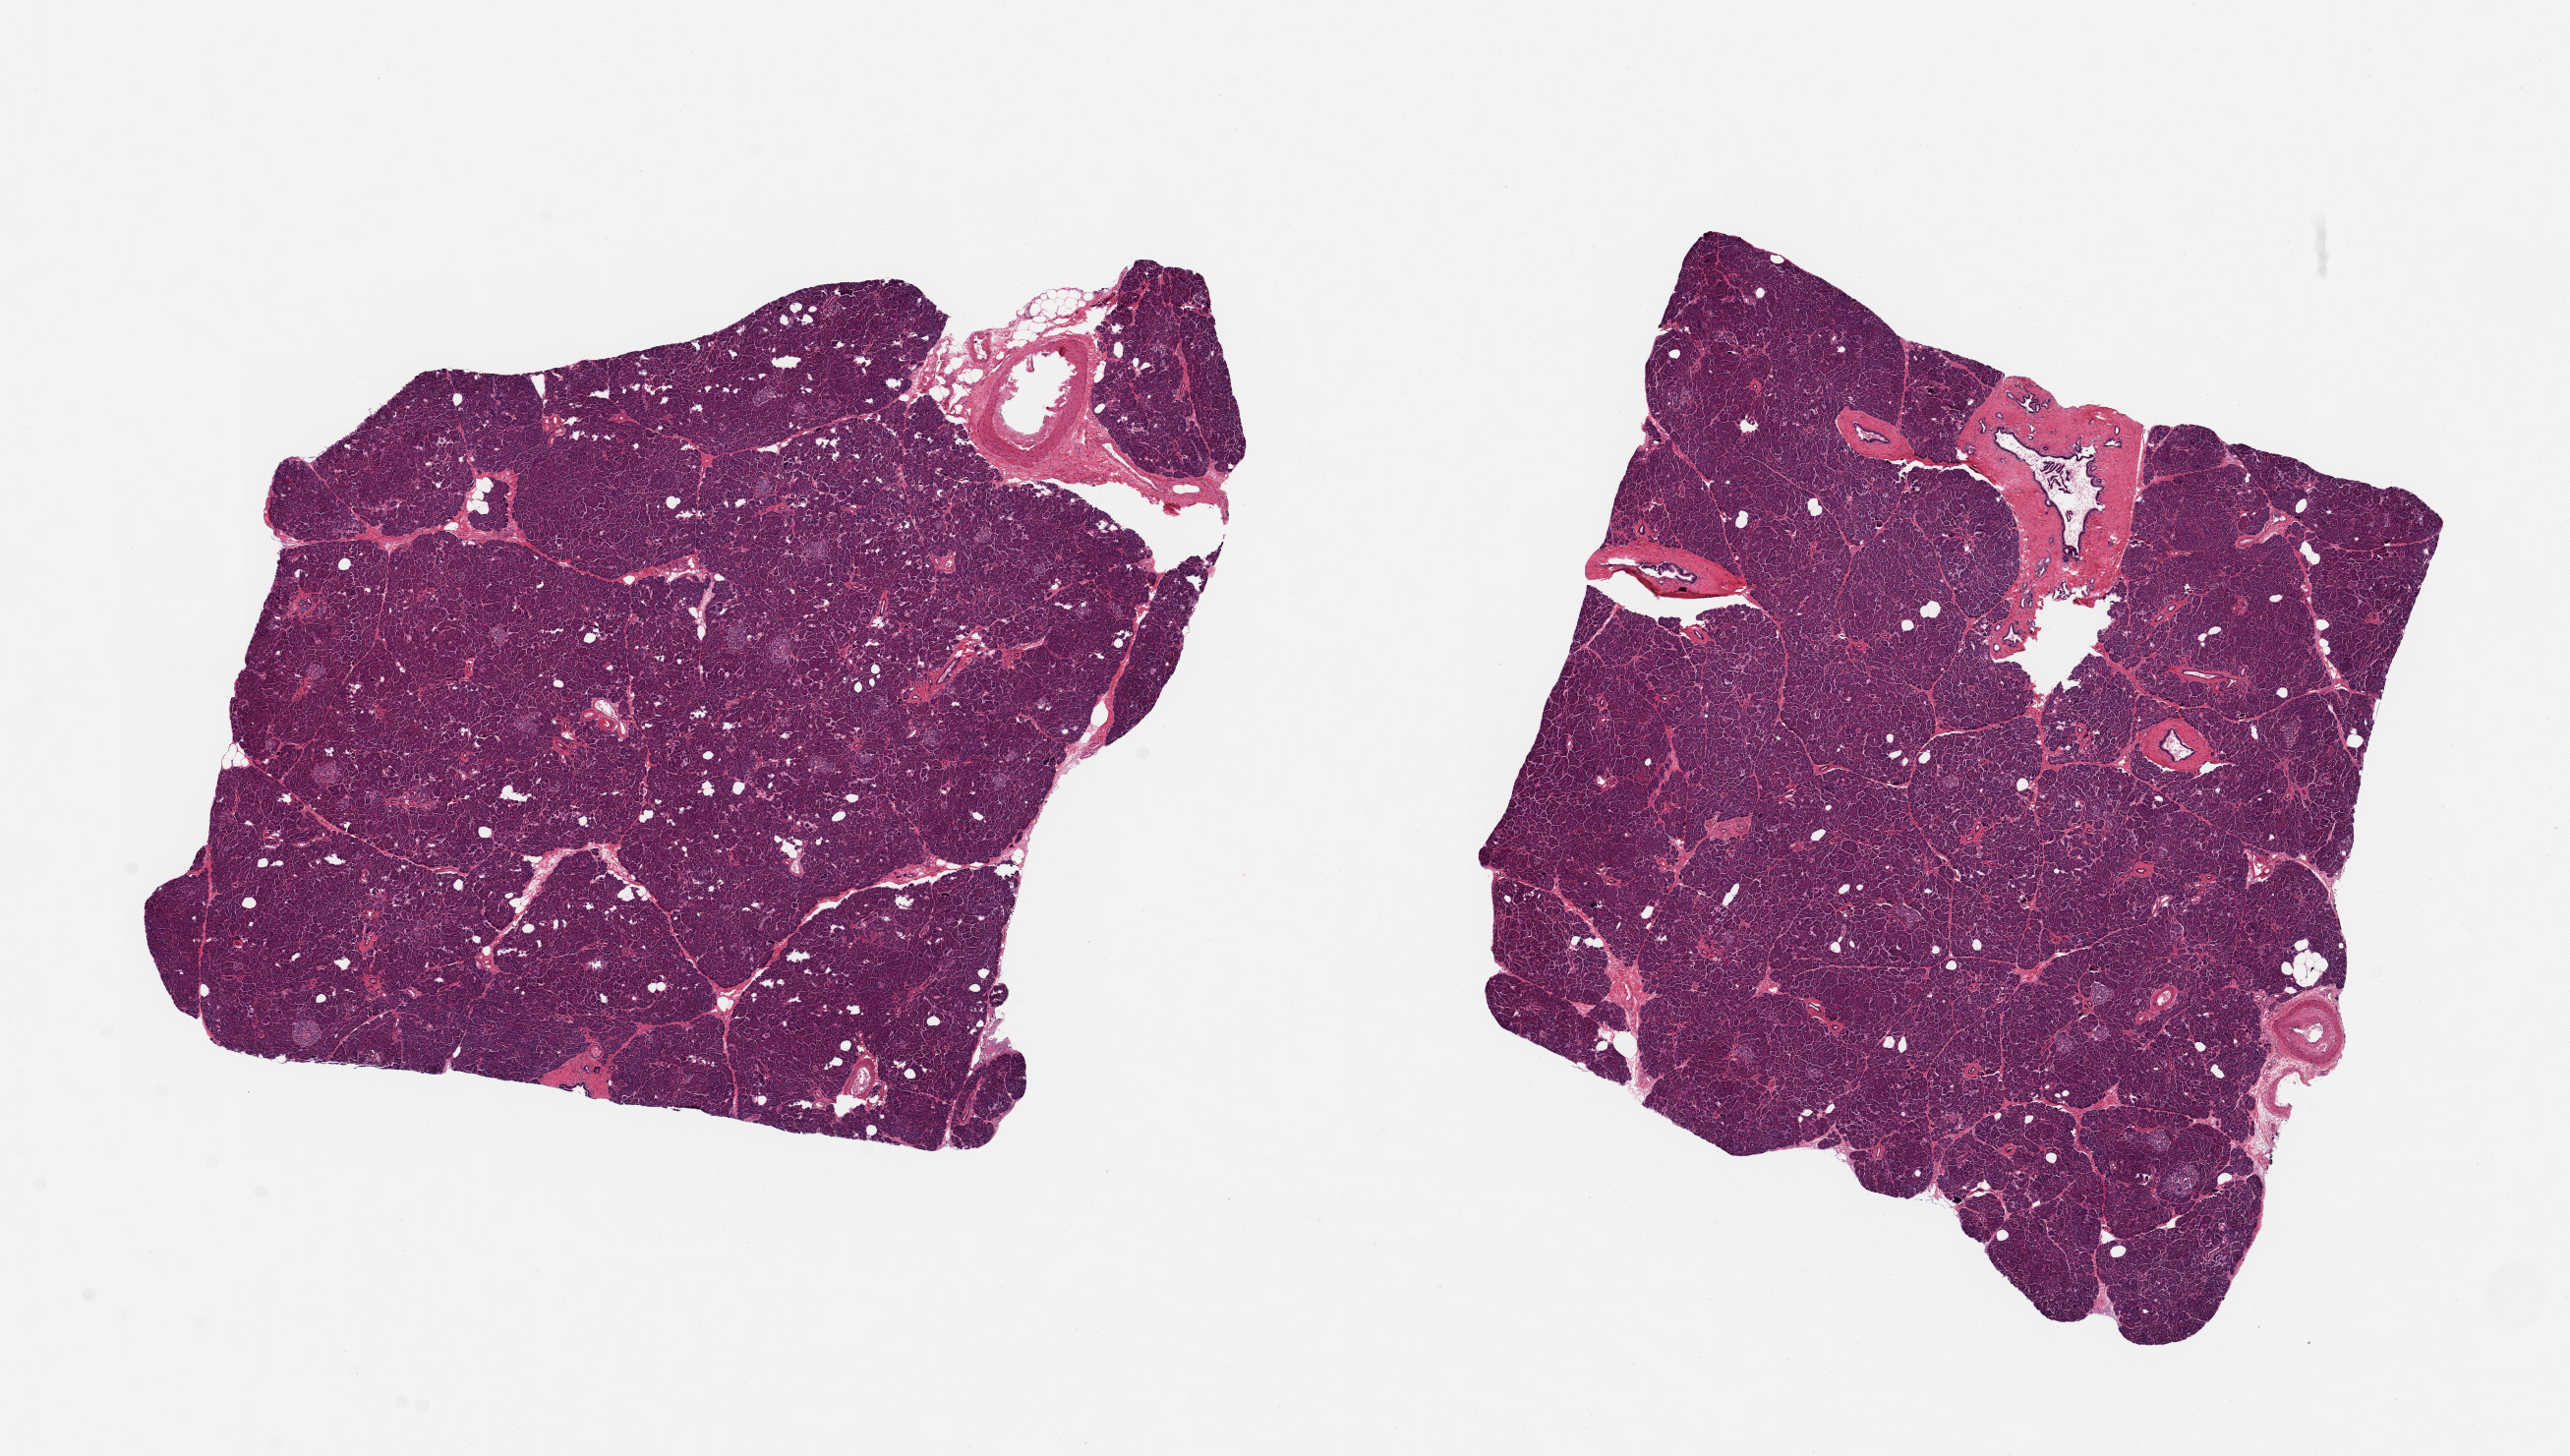
Digitized hematoxylin and eosin (H&E)-stained section, a low-resolution overview of the entire scanned area, about 20.7 x 11.7 mm; PAXgene-fixed paraffin-embedded (PFPE) section; target tissue: pancreas; tissue donor sample. Donor: female.
Review note (as recorded): 2 ~ 7x6mm pieces, clean specimens, no fat.